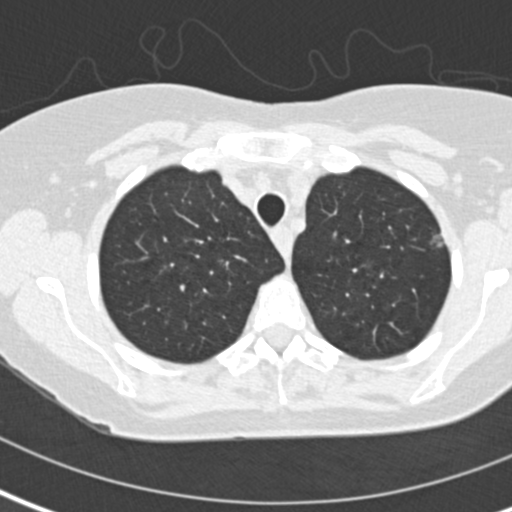
Chest CT (low-dose screening protocol), one axial image. Second annual screen. Lung window (W 1500 / L -600 HU). 2 mm slice thickness. 512 × 512 image matrix, field of view 280 × 280 mm. Female participant, aged 60 years at enrolment. Former smoker at enrolment.
- Lesion marked by an expert reader, bounding box (x1, y1, x2, y2) in pixels: (416, 224, 463, 265).
- The screening reader recorded 2 non-calcified nodules or masses ≥4 mm on this exam; which of them this box marks is not recorded.
- Official screen result: positive, change unspecified: nodule(s) >= 4 mm or enlarging nodule(s), mass(es), or other non-specific abnormalities suspicious for lung cancer.